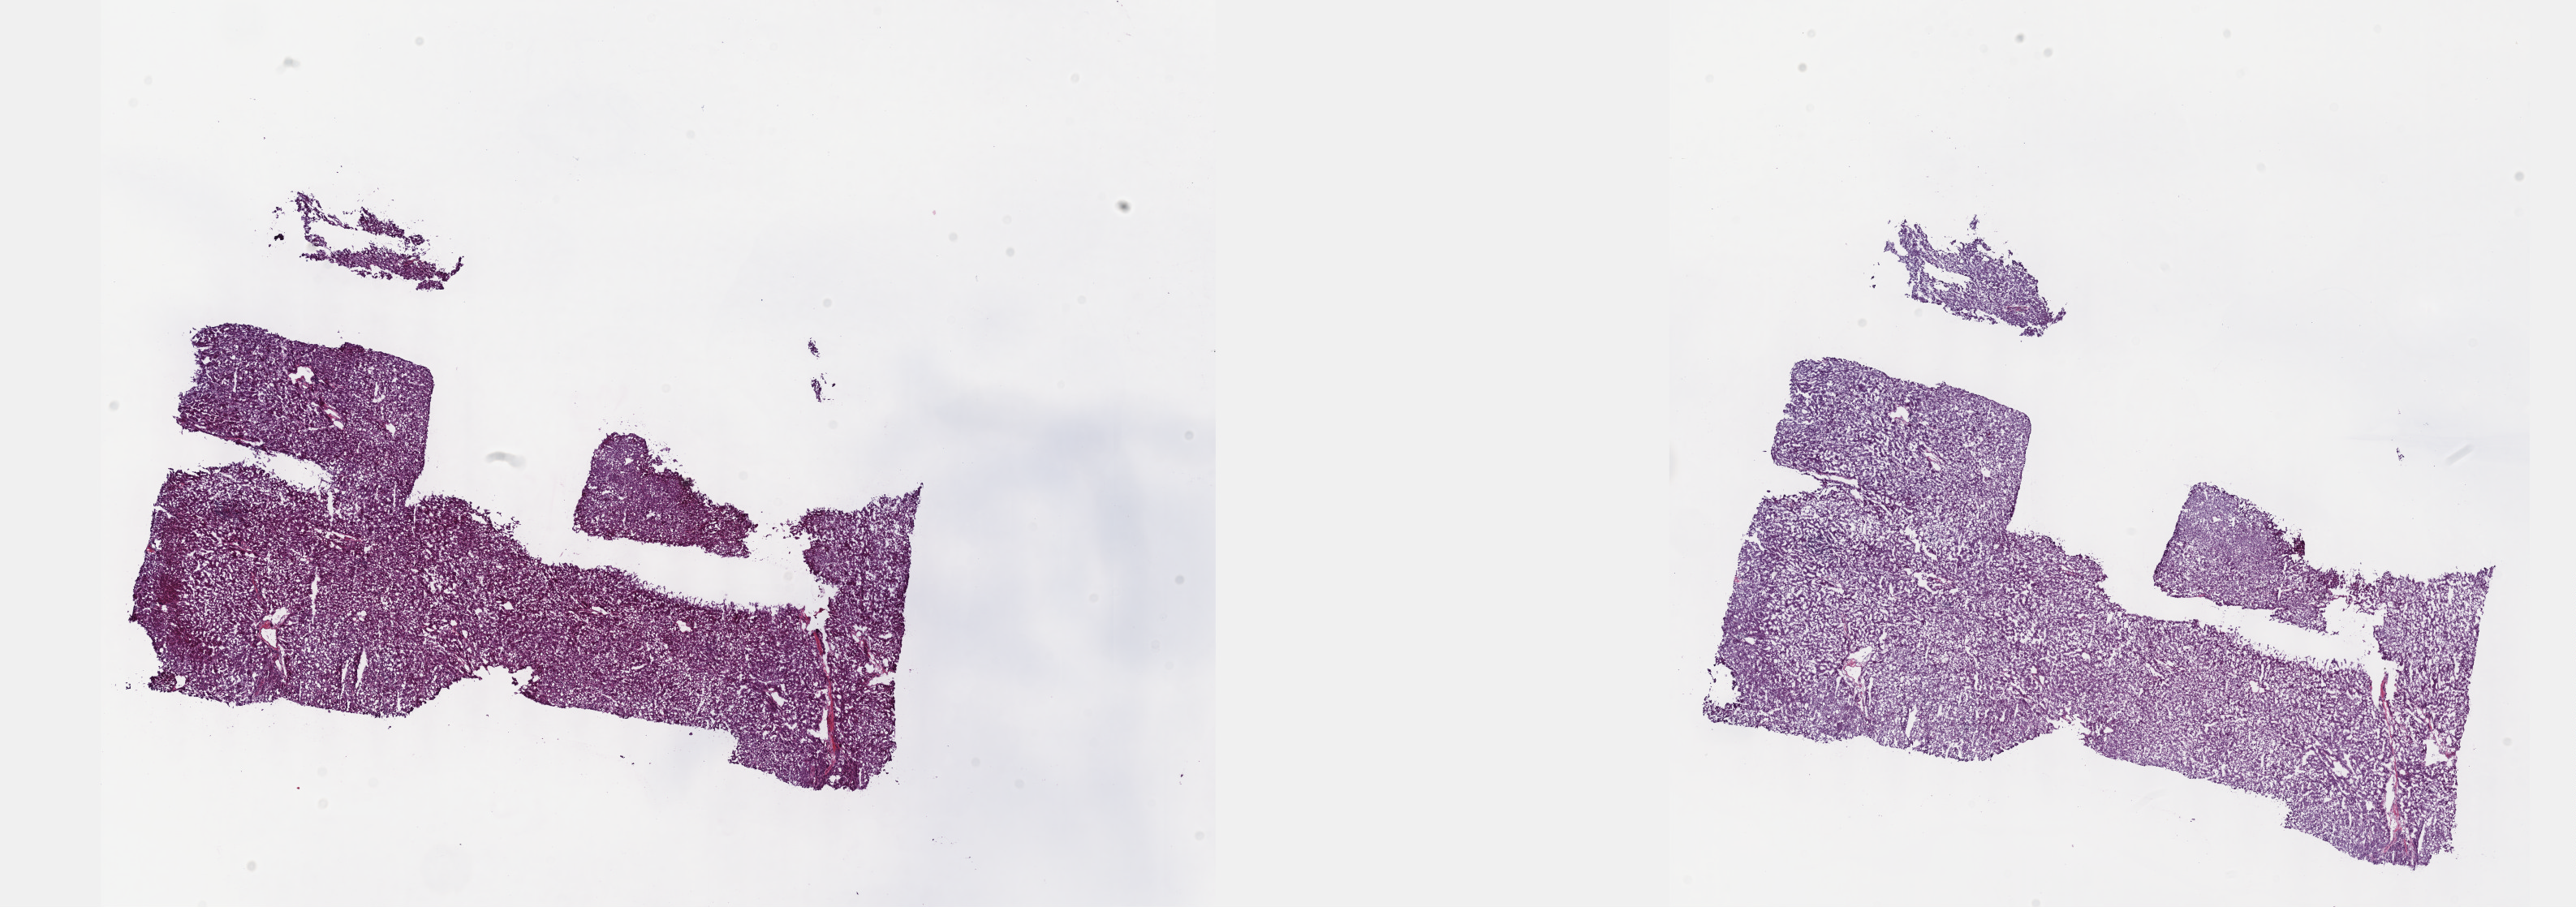
Whole-slide histology image, H&E-stained, low-resolution overview of the scanned area, about 25.7 x 9.0 mm; frozen section; primary tumour sample from the liver. Male, age 68 years at initial diagnosis. Histologic grade: G2 (moderately differentiated). Slide review estimates, as recorded: tumour cells 96%, tumour nuclei 97%, normal cells 0%, stromal cells 3%, necrosis 1%. Inflammatory infiltration, as recorded: lymphocyte infiltration 2%, monocyte infiltration 0%, neutrophil infiltration 0%.
* TNM: T3a N0 M0
* AJCC pathologic stage: IIIA (7th edition)
* histologic diagnosis: Hepatocellular carcinoma, NOS